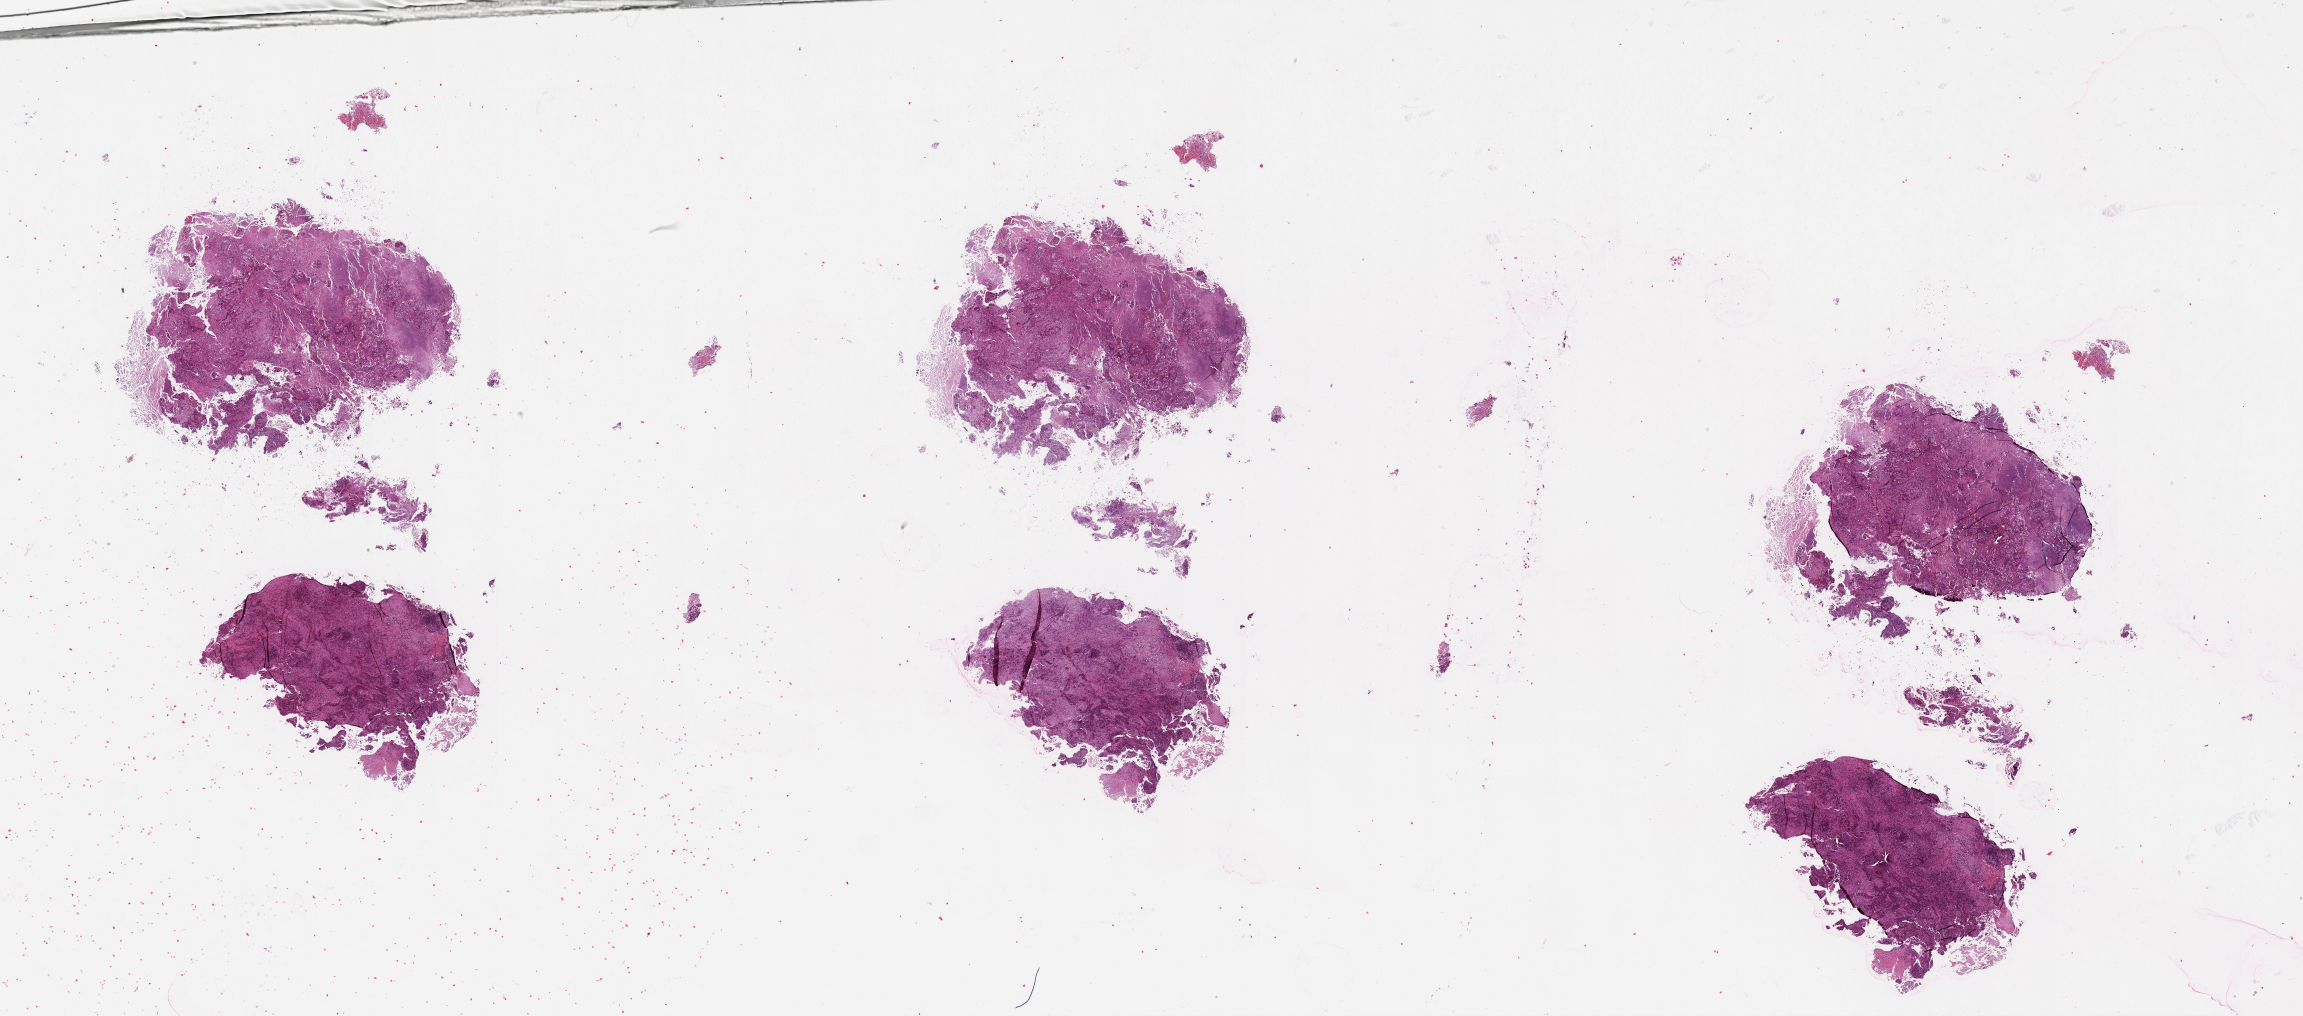
H&E whole-slide image, low-resolution overview of the scanned area, about 37.1 x 16.4 mm. Lung, tissue type not recorded.
• patient diagnosis (cohort enrolment): lung adenocarcinoma (lung)